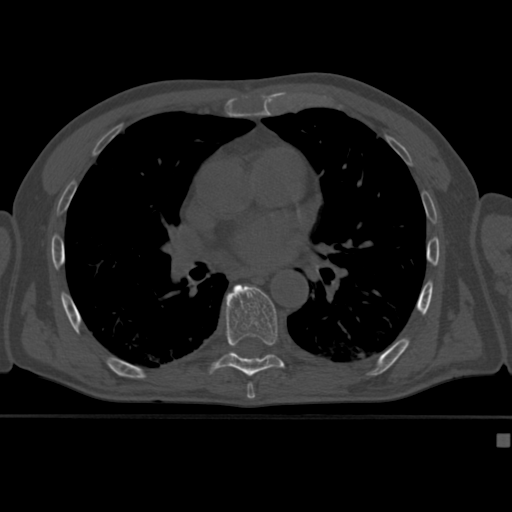
CT including the spine, one axial slice; slice 264 of 430 in the series (ordered by position); reconstruction kernel Br40s; bone window (W 1800 / L 400 HU); 512 × 512 image matrix, field of view 337 × 337 mm. Patient: male, 64 years. From the clinical record (not read from this slice): primary cancer: uterus; vertebrae with lytic lesions (as recorded): T1, T4, T5, T7, L5.
Outlined on this slice (semi-automatically segmented with operator editing):
- T8 vertebra: bounding box [x1, y1, x2, y2] px = [209, 284, 285, 377]